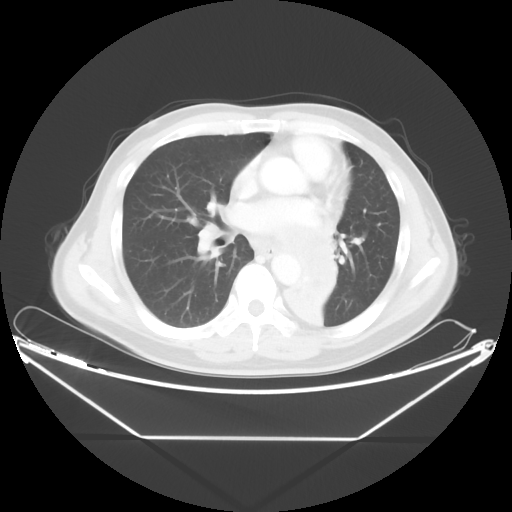
Chest CT, one axial slice; position 23 of 48 along the scan axis; reconstruction kernel STANDARD; lung window (W 1500 / L -600 HU); 512 × 512 image matrix, field of view 438 × 438 mm. Patient: male, 58 years. From the clinical record (not read from this slice): clinical TNM (as recorded): T3 N3 M0.
Outlined on this slice (rectangle marked by the reading radiologist):
- lung tumour (recorded histology: squamous cell carcinoma): bounding box [x1, y1, x2, y2] px = [275, 221, 347, 330]